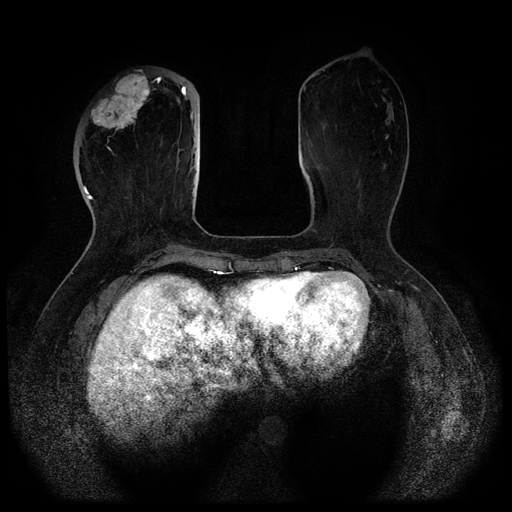
Breast MRI (dynamic contrast-enhanced, multi-phase), one axial slice. Position 32 of 116 along the scan axis. Dynamic contrast-enhanced series, time point 2 of 5 at this slice position (early post-contrast). 1.5 T. TE 2.6 ms, TR 5.3 ms. 512 × 512 image matrix, field of view 350 × 350 mm. Patient: female, 51 years.
Structures marked on this image (semi-automatically segmented with operator editing):
- breast lesion (labelled 'tumour' in the annotation; benign lesions carry a separate 'benign' label): bounding box (x1, y1, x2, y2) in pixels: (90, 69, 153, 132)